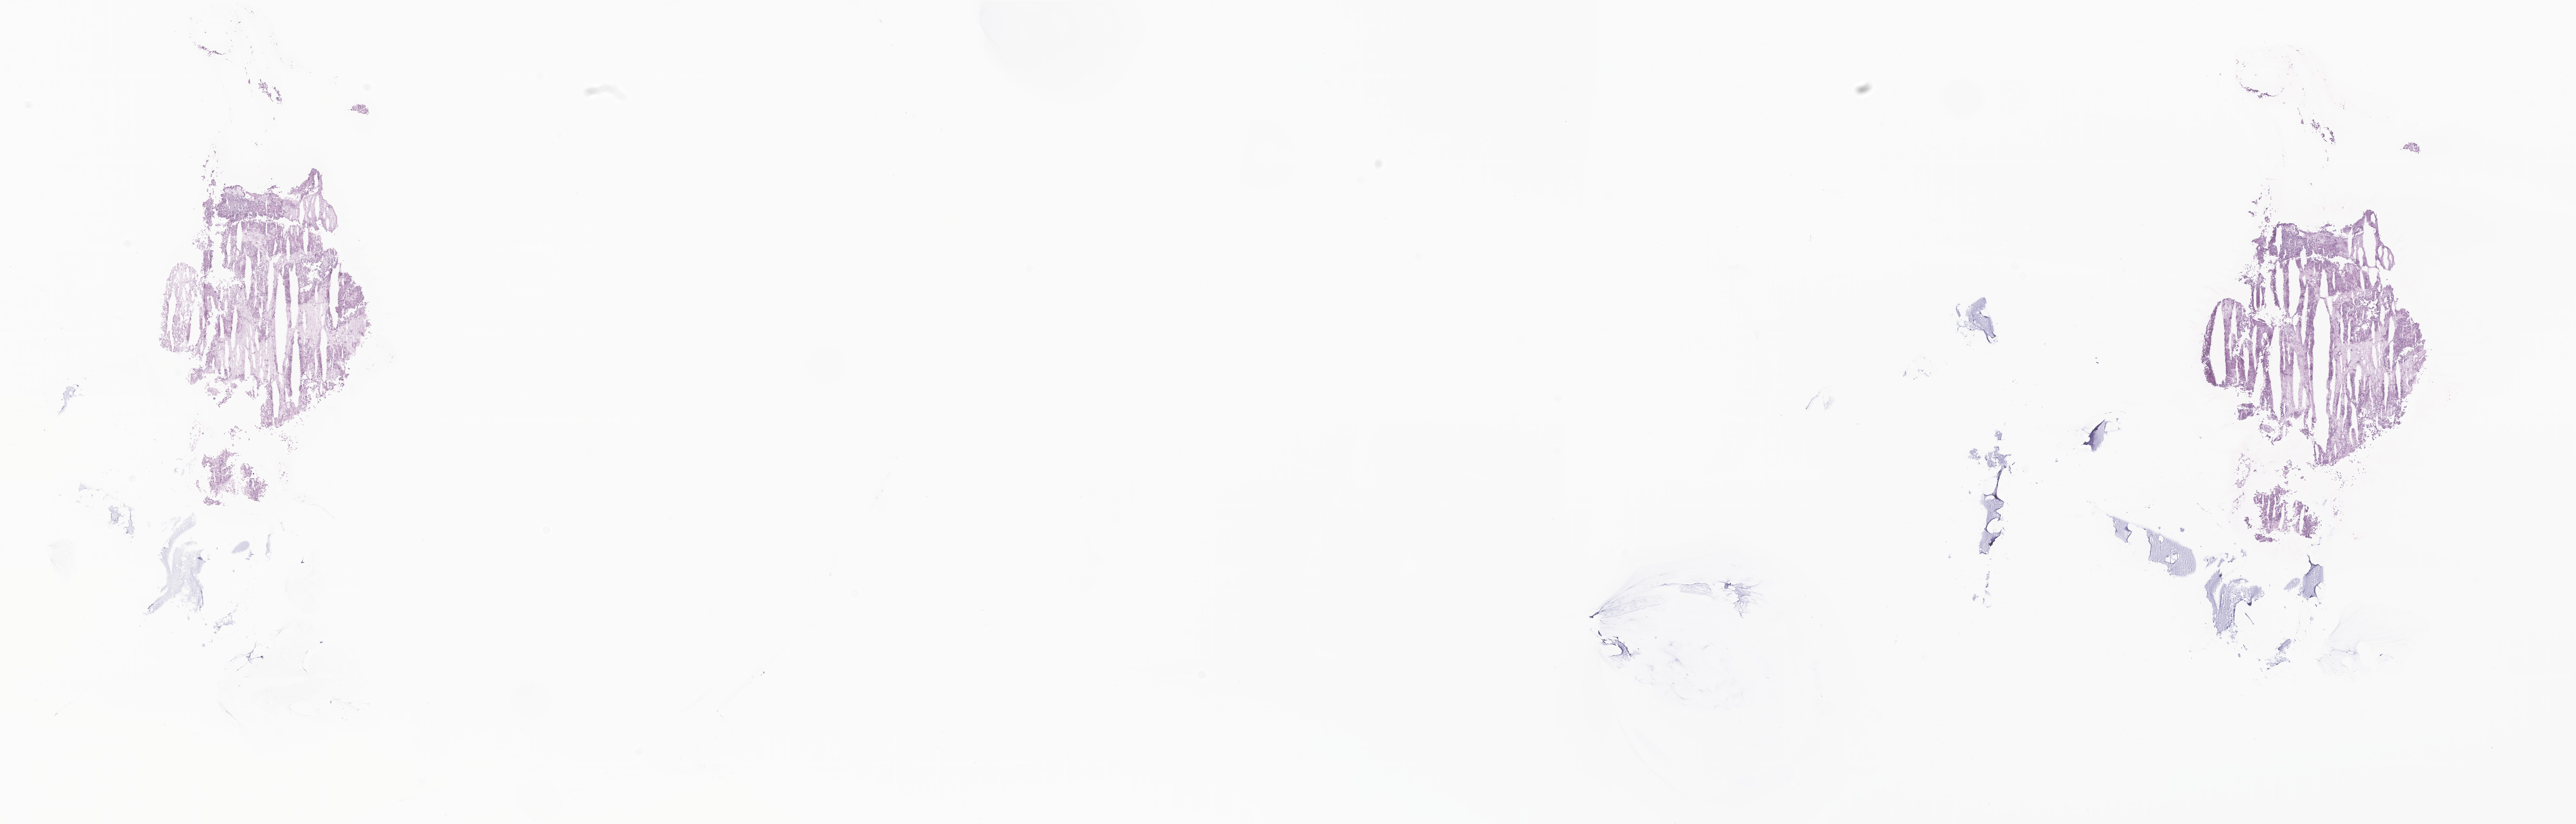
Whole-slide image, H&E stain of tumor tissue from the brain — whole scanned area (about 32.0 x 10.2 mm) shown as a low-resolution overview; frozen section. Patient female; age 302 days.
Diagnosis (ICD-O-3 morphology term): Choroid plexus papilloma, NOS.